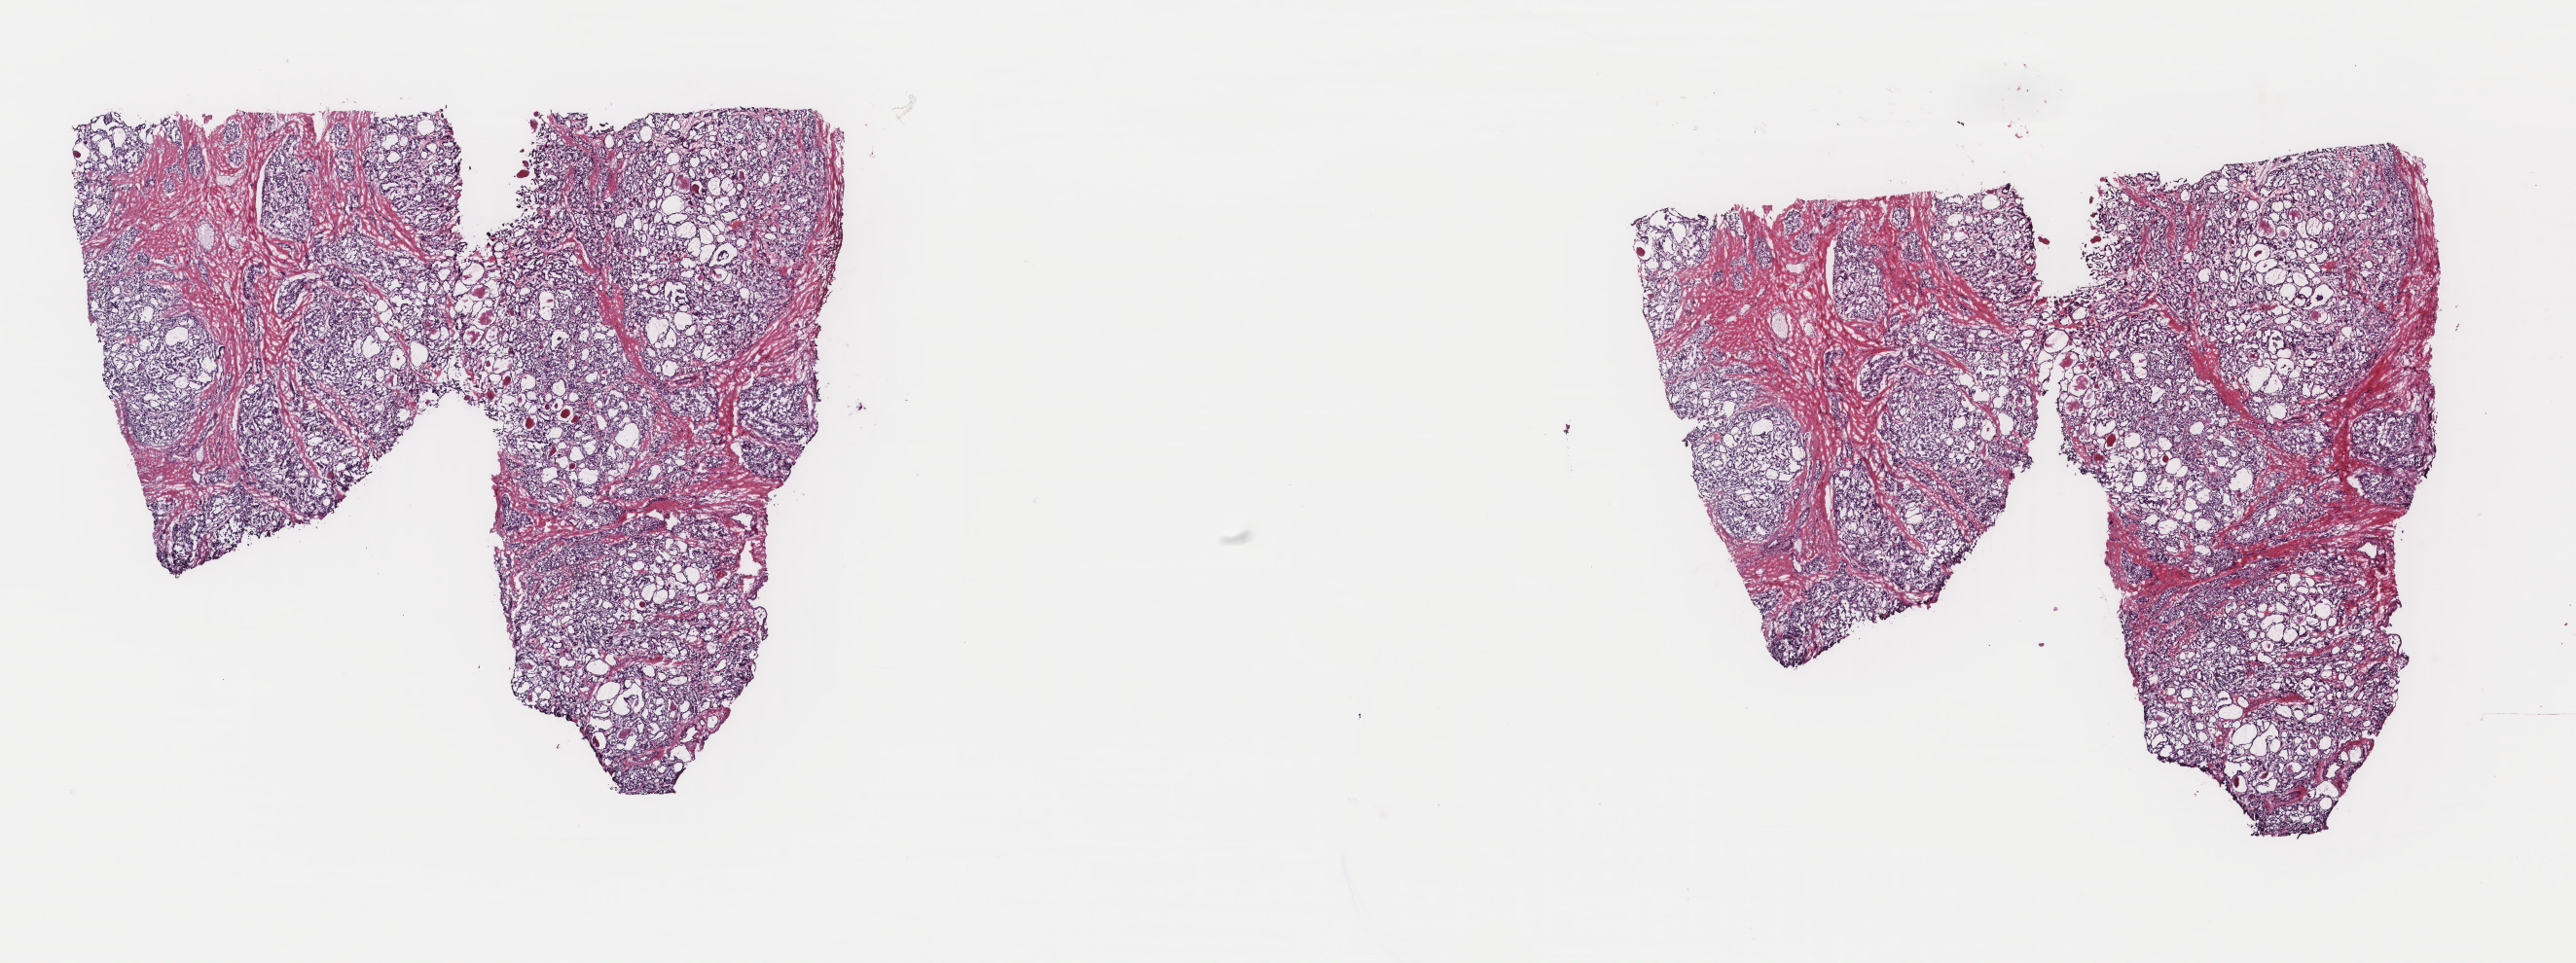
Digitized H&E-stained tissue section (whole slide) — low-resolution overview of the scanned area, about 21.0 x 7.9 mm, frozen section from the top of the tissue portion, thyroid, primary tumour sample. Patient: female, age at initial diagnosis 47 years. Composition of this section per pathologist review: tumour cells 85%, tumour nuclei 90%, normal cells 0%, stromal cells 15%, necrosis 0%. Infiltration values recorded for this section: lymphocyte infiltration 0%, monocyte infiltration 0%, neutrophil infiltration 0%.
* TNM: T2 N1a MX
* lymph nodes positive (case pathology): 4 of 30 examined
* AJCC pathologic stage: III (7th edition)
* pathologic diagnosis: Papillary carcinoma, follicular variant (thyroid gland)